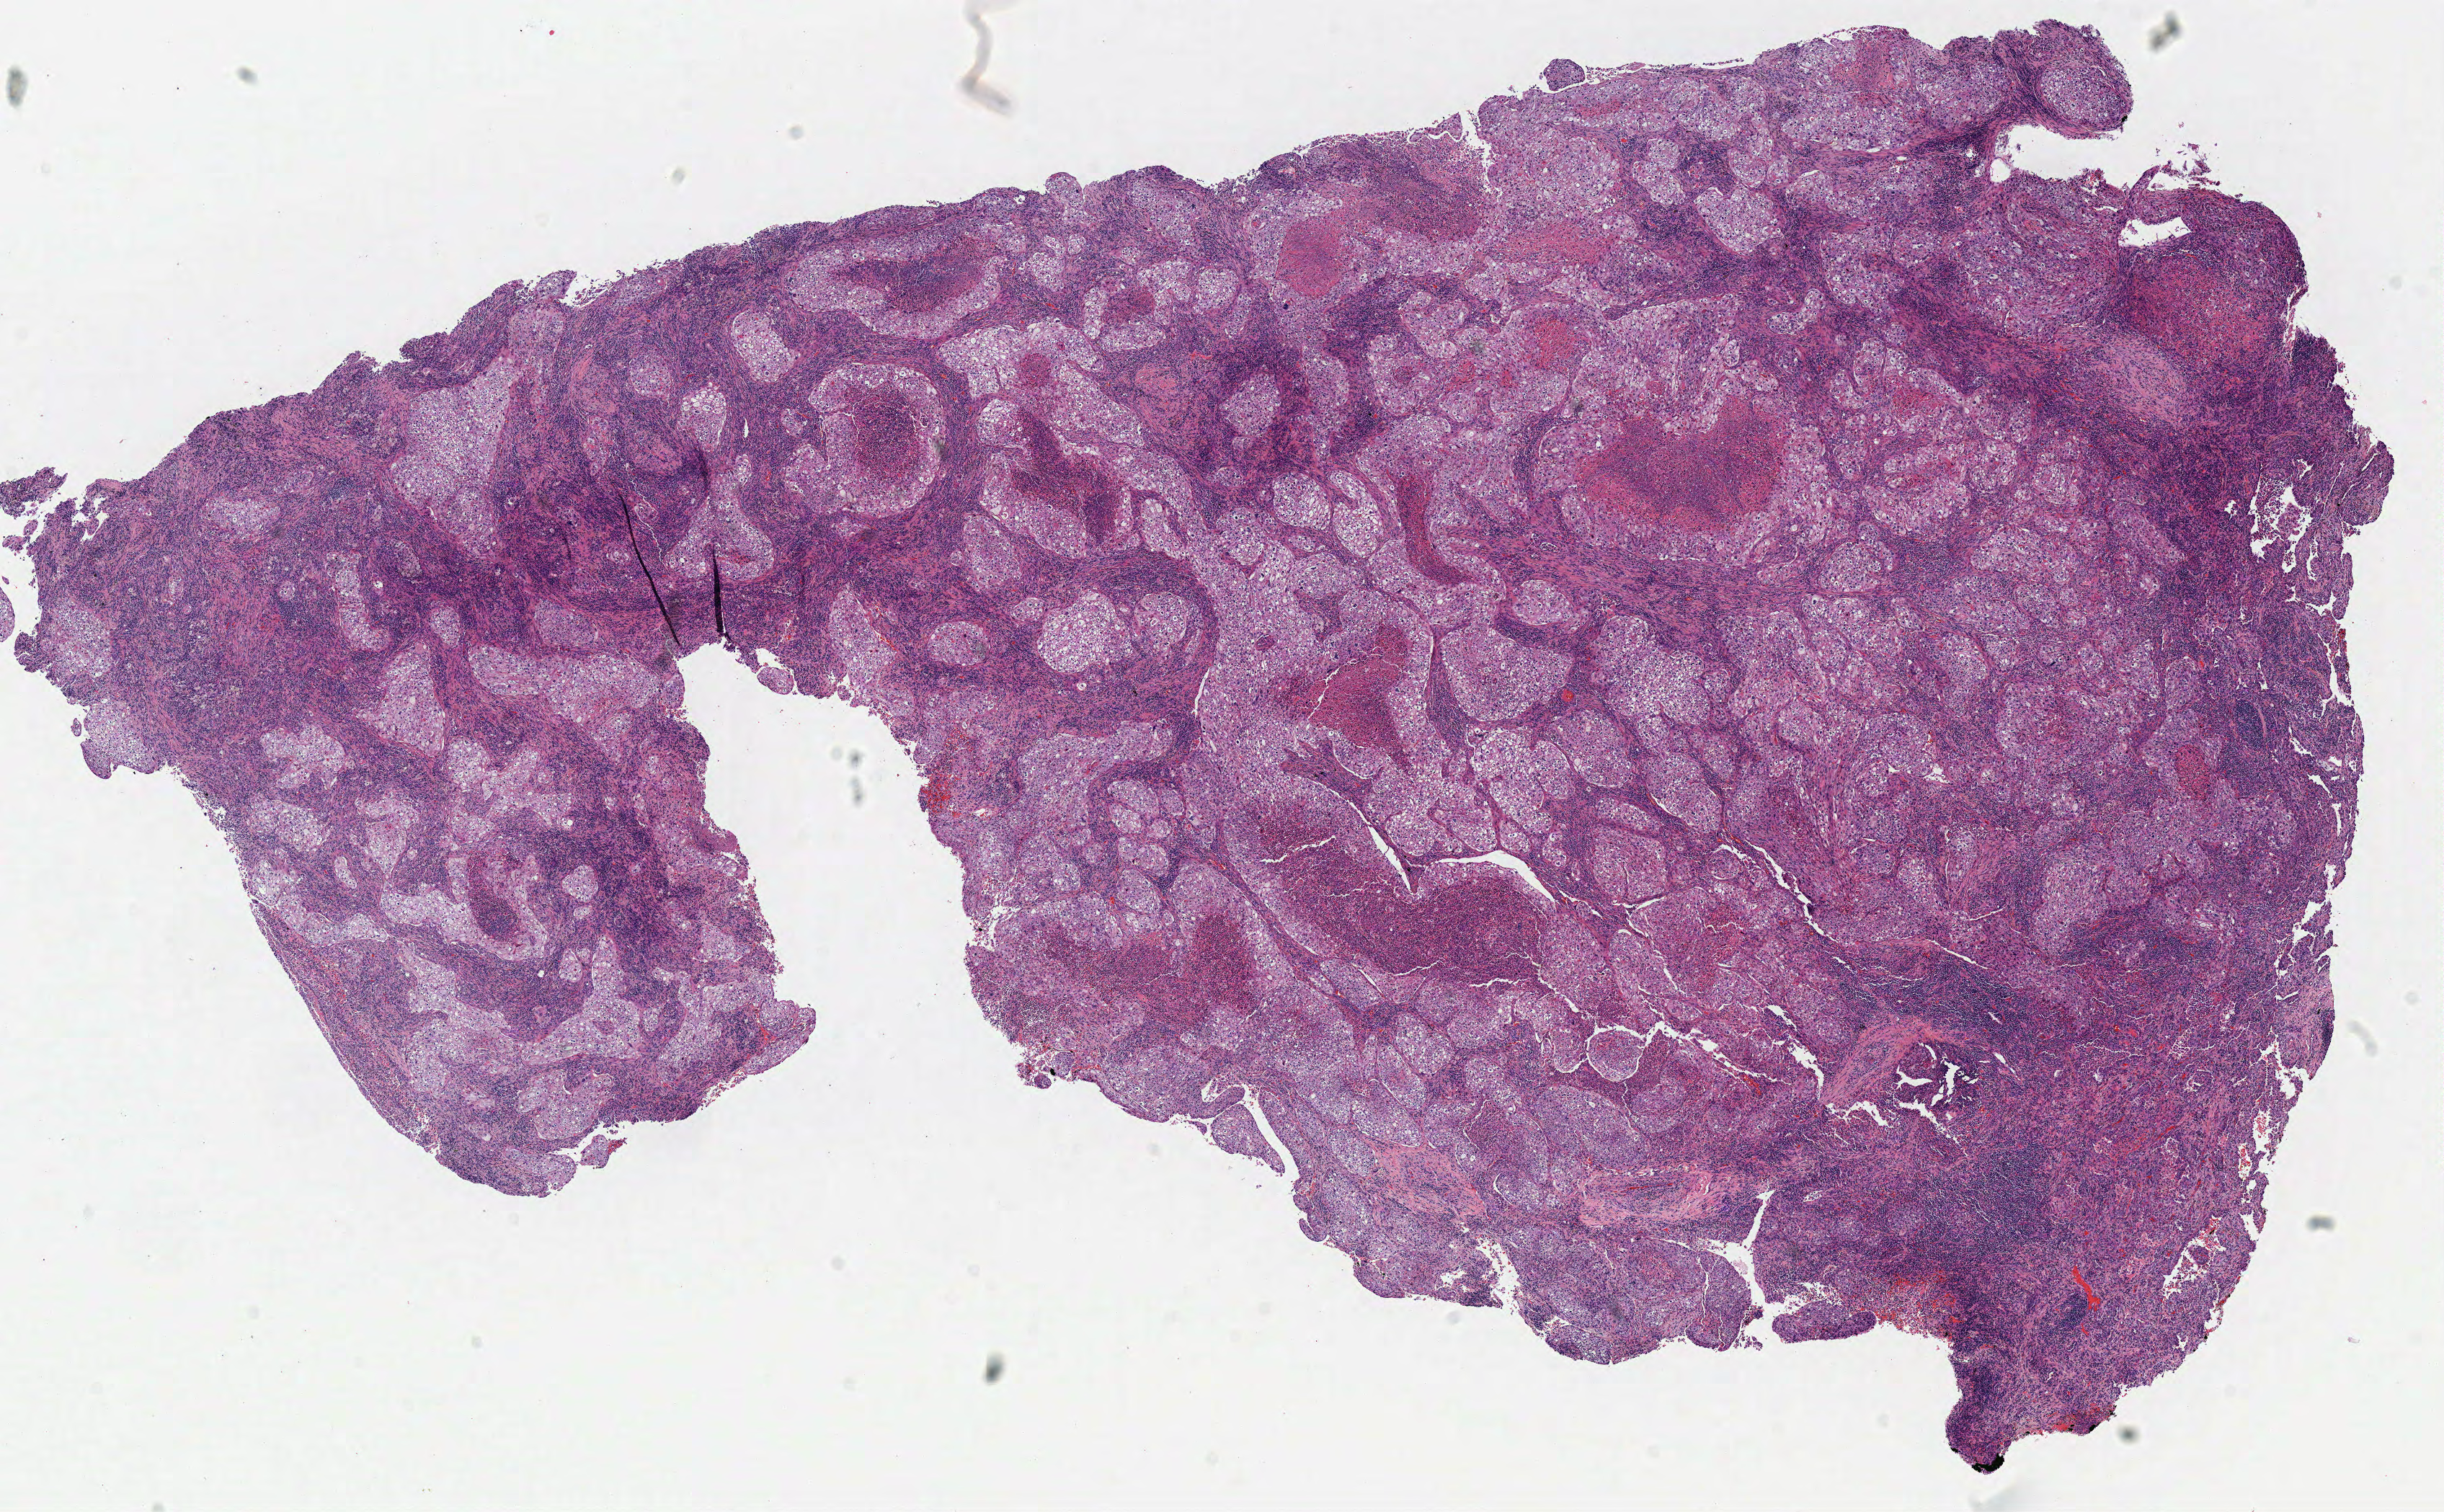
Digitized H&E tissue section (whole slide), shown as a low-resolution overview of the whole scanned area (about 13.4 x 8.3 mm). Frozen section. Sample: primary tumour, lung. Male, age 64 years at initial diagnosis. Composition of this section per pathologist review: tumour cells 80%, tumour nuclei 65%, normal cells 0%, stromal cells 5%, necrosis 15%.
• histologic diagnosis: Squamous cell carcinoma, NOS (overlapping lesion of lung)
• laterality: right
• AJCC pathologic stage: IIB (7th edition)